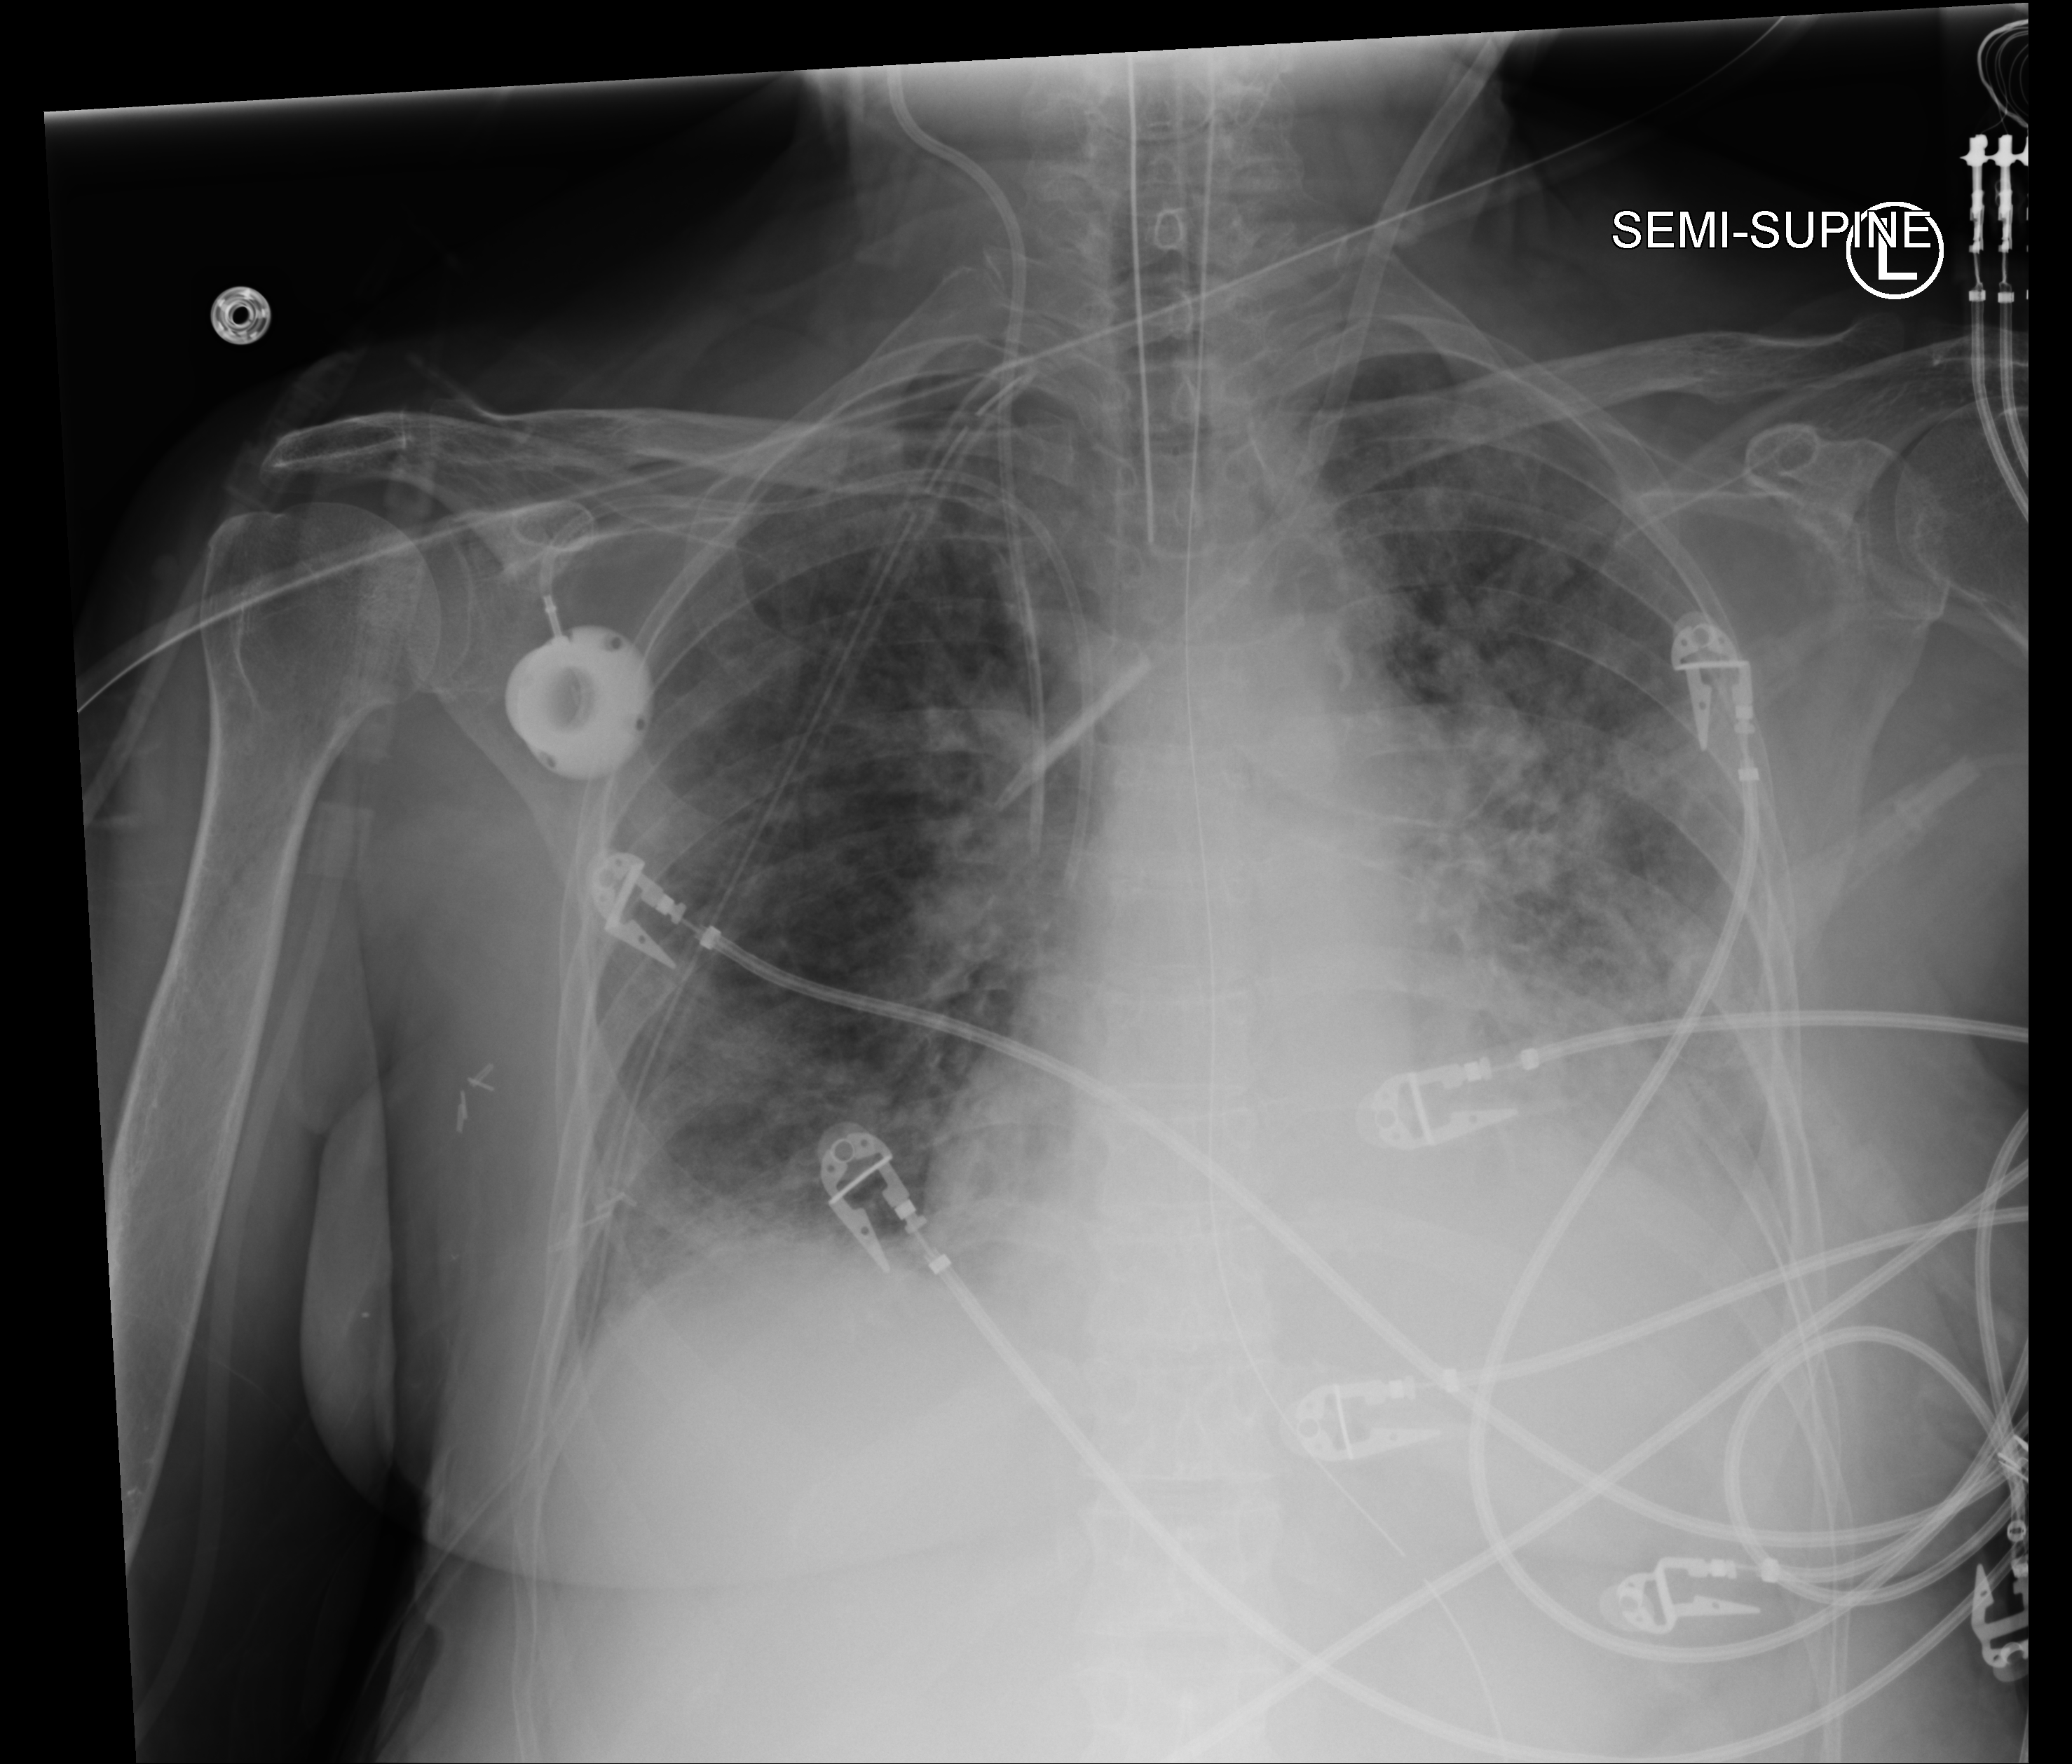
Chest X-ray (portable). Patient hospitalised with COVID-19; female, aged 60–74 years.
From the hospital-stay record, not from the radiograph (when in the stay this image was taken is not recorded):
- admitted to intensive care during this hospital stay: yes